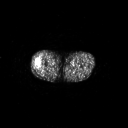
FDG PET of an extremity soft-tissue mass (from a PET/CT study), one axial slice. Slice 231 of 267 in the series (ordered by position). 3.27 mm slice thickness. 128 × 128 image matrix, field of view 700 × 700 mm. Male patient, age 43 years. From the clinical record (not read from this slice): histological type: poorly differentiated synovial sarcoma; grade: high; site of the primary tumour: right buttock.
Annotated regions visible in this slice (expert contour drawn on MRI and transferred to this co-registered scan by the dataset authors):
- gross tumour volume including surrounding oedema: bounding box (x1, y1, x2, y2) in pixels: (34, 58, 44, 69)
- gross tumour volume (mass): (34, 59, 42, 69)